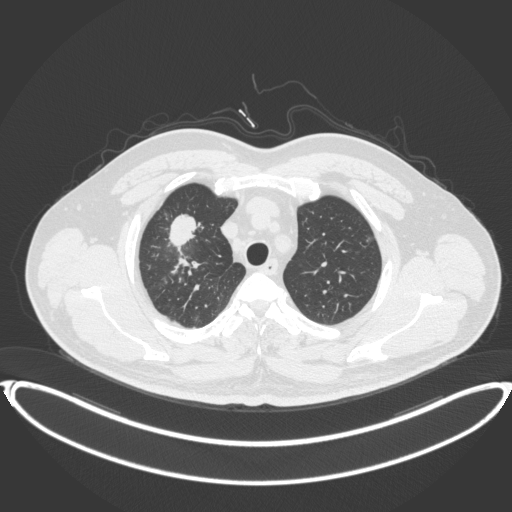
Chest CT, one axial slice; slice 314 of 399 in the series (ordered by position); reconstruction kernel B31f; lung window (W 1500 / L -600 HU); 1 mm slice thickness; 512 × 512 image matrix, field of view 445 × 445 mm. Patient: male, 53 years. From the clinical record (not read from this slice): clinical TNM (as recorded): T2a N0 M0.
Outlined on this slice (rectangle marked by the reading radiologist):
- lung tumour (recorded histology: adenocarcinoma): bounding box <164,209,202,250> (left, top, right, bottom; pixels)